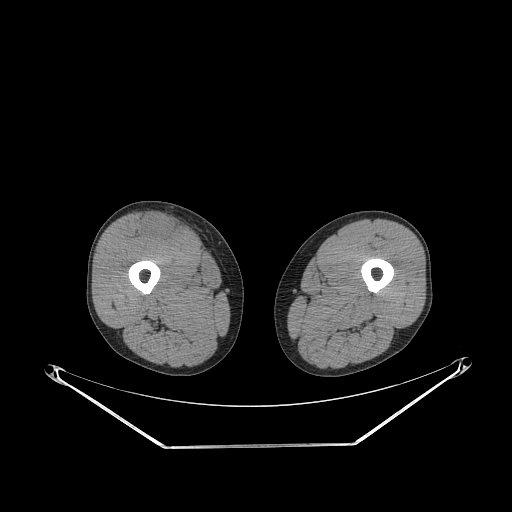
CT of an extremity soft-tissue mass (from a PET/CT study), one axial slice; slice 250 of 311 in the series (ordered by position); reconstruction kernel STANDARD; 140 kVp; soft-tissue window (W 400 / L 40 HU); 3.75 mm slice thickness; 512 × 512 image matrix, field of view 500 × 500 mm. Male patient. Case-level facts recorded for this patient, not image findings: histological type: pleiomorphic leiomyosarcoma; grade: intermediate; site of the primary tumour: right thigh.
Structures marked on this image (expert contour drawn on MRI and transferred to this co-registered scan by the dataset authors):
- gross tumour volume including surrounding oedema: bounding box <142,214,181,241> (left, top, right, bottom; pixels)